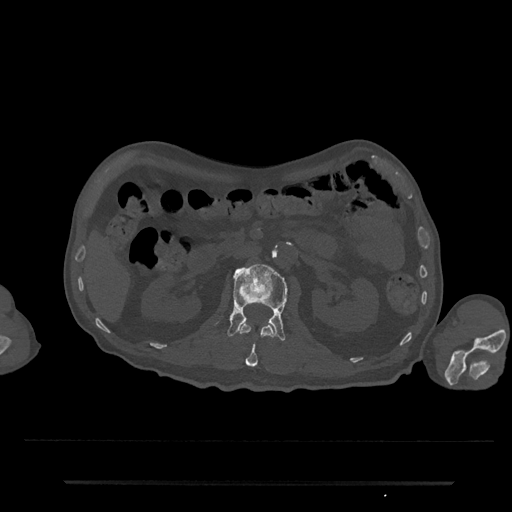
CT including the spine, one axial slice. Position 88 of 797 along the scan axis. Reconstruction kernel Br40s/3. 120 kVp. Bone window (W 1800 / L 400 HU). 512 × 512 image matrix. Patient: male, 74 years. From the clinical record (not read from this slice): primary cancer: prostate.
Structures marked on this image (semi-automatically segmented with operator editing):
- L1 vertebra: bounding box [x1, y1, x2, y2] px = [239, 322, 274, 367]
- L2 vertebra: [227, 264, 288, 341]